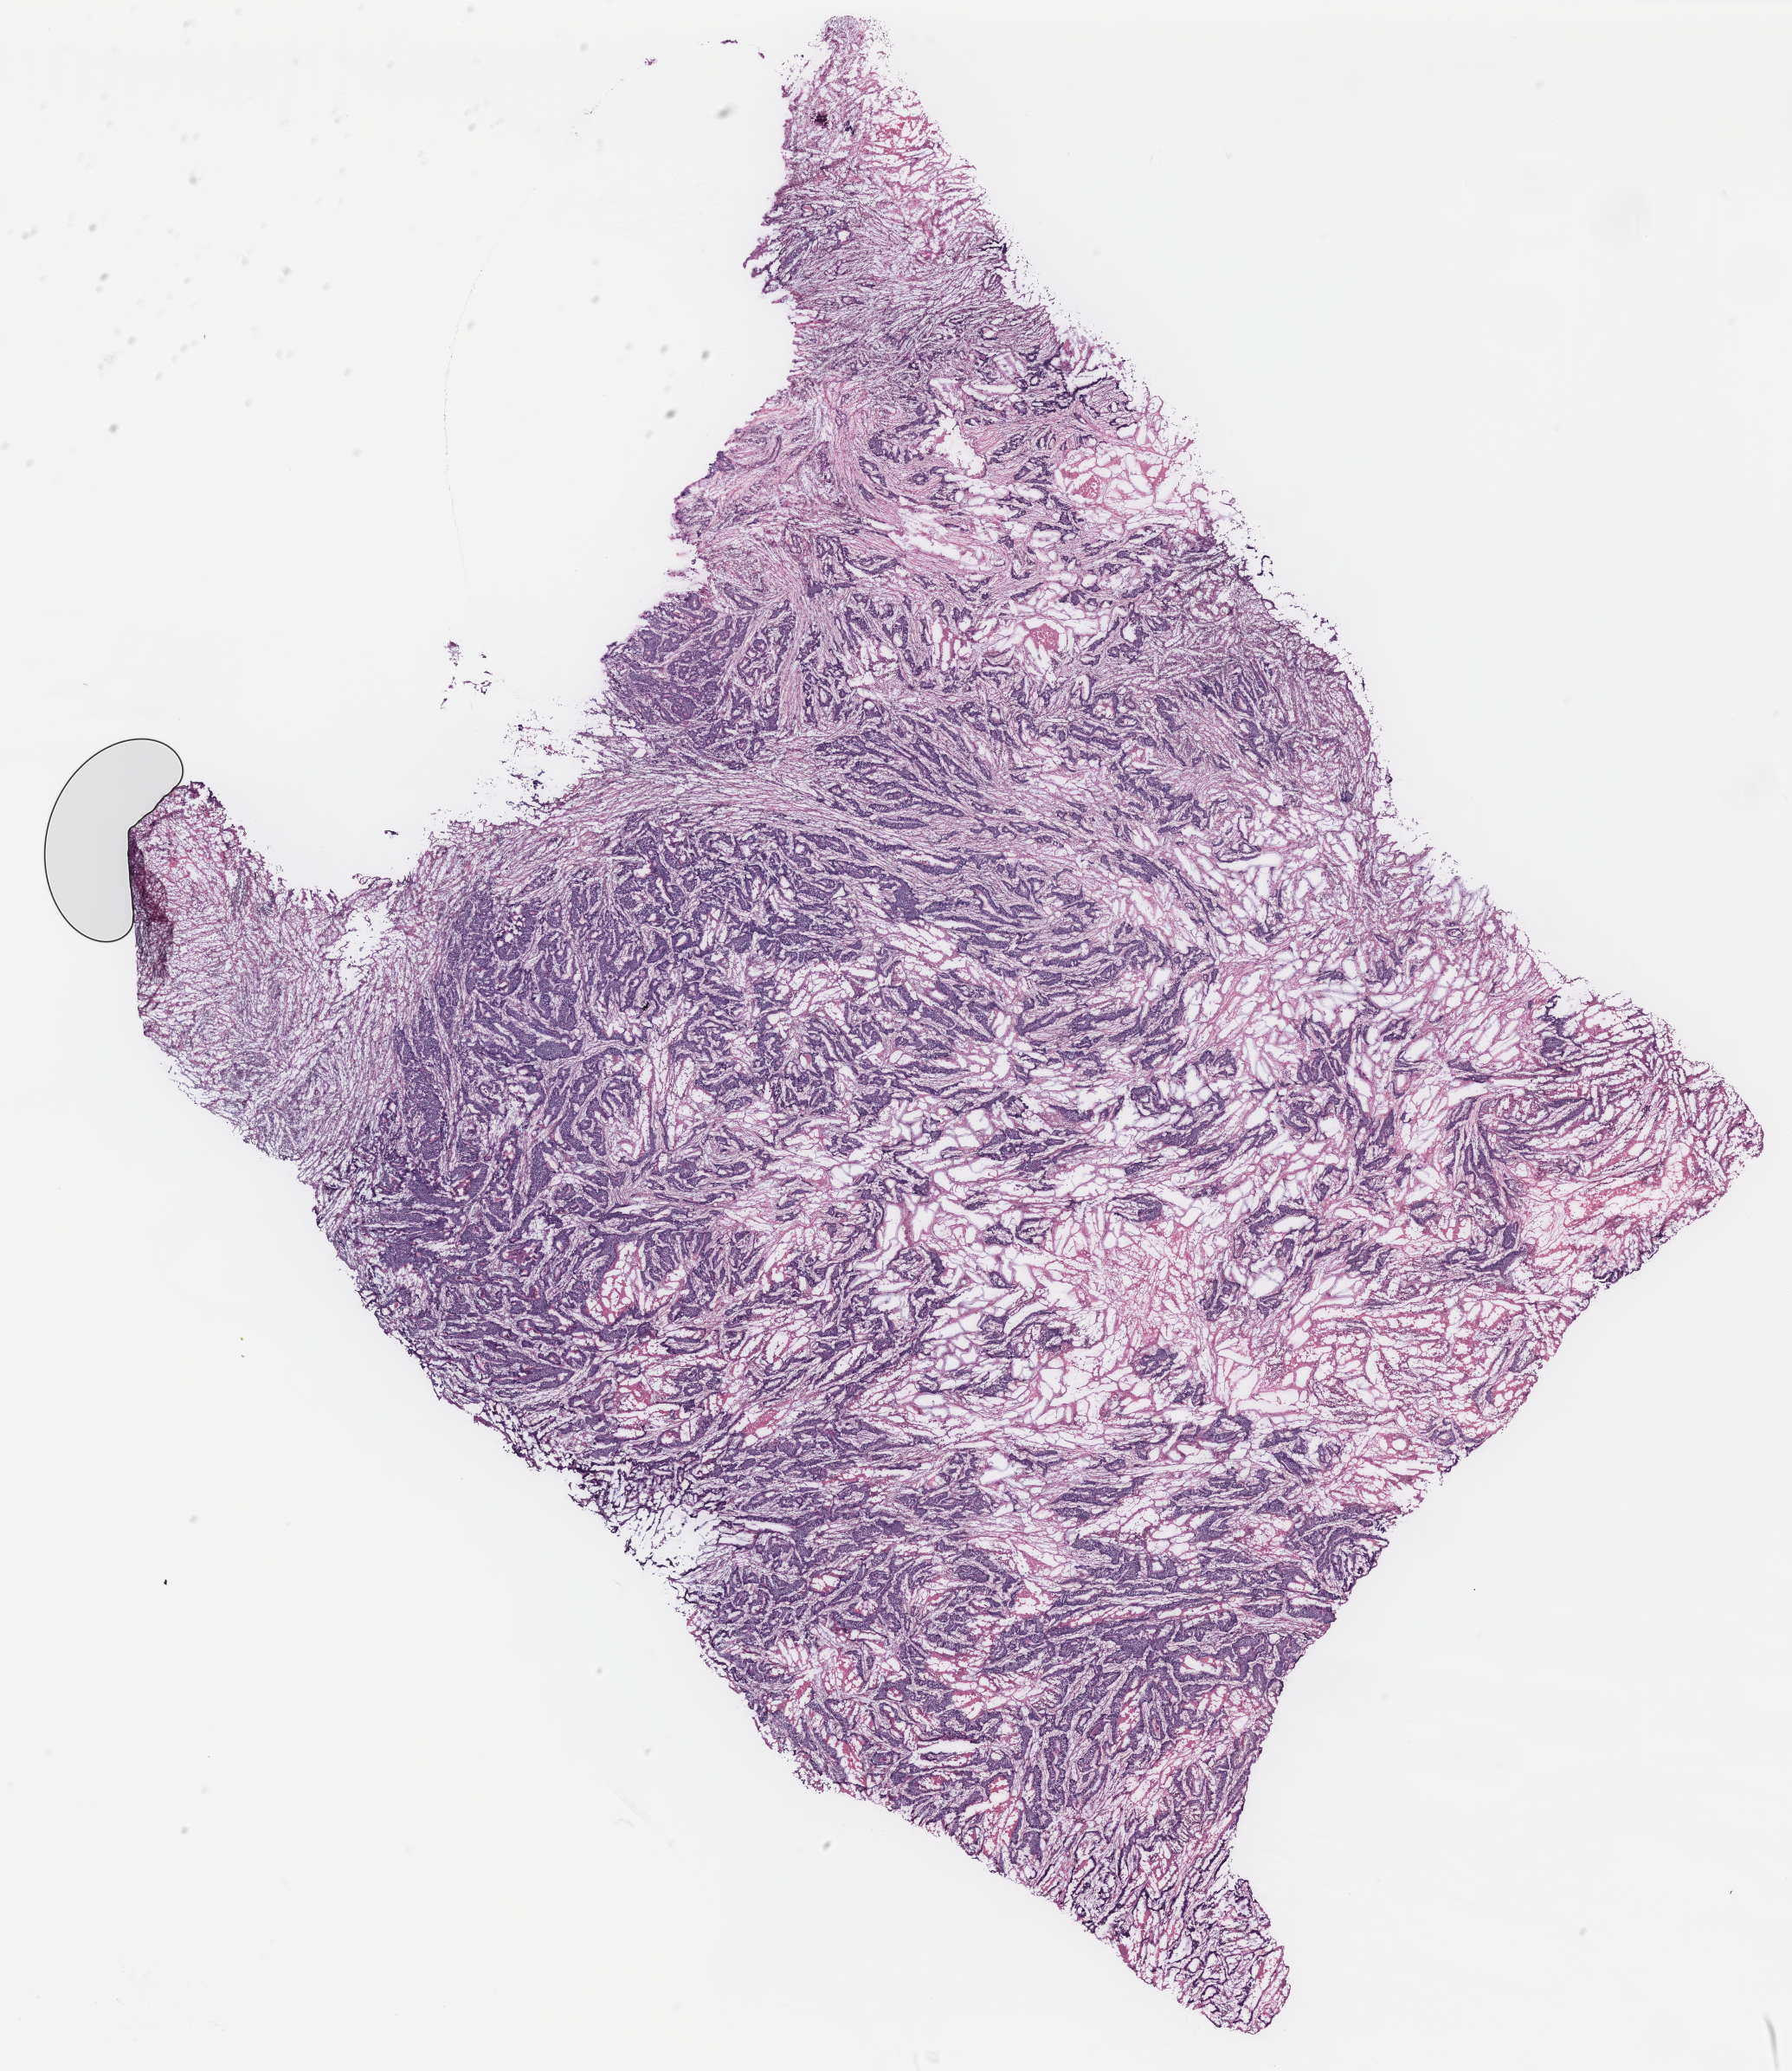
Digitized H&E-stained tissue section (whole slide) — a low-resolution overview of the entire scanned area, about 16.6 x 19.1 mm (slide scanned at 40x). Colon, tissue type not recorded.
Patient diagnosis (cohort enrolment): colon cancer (colon).